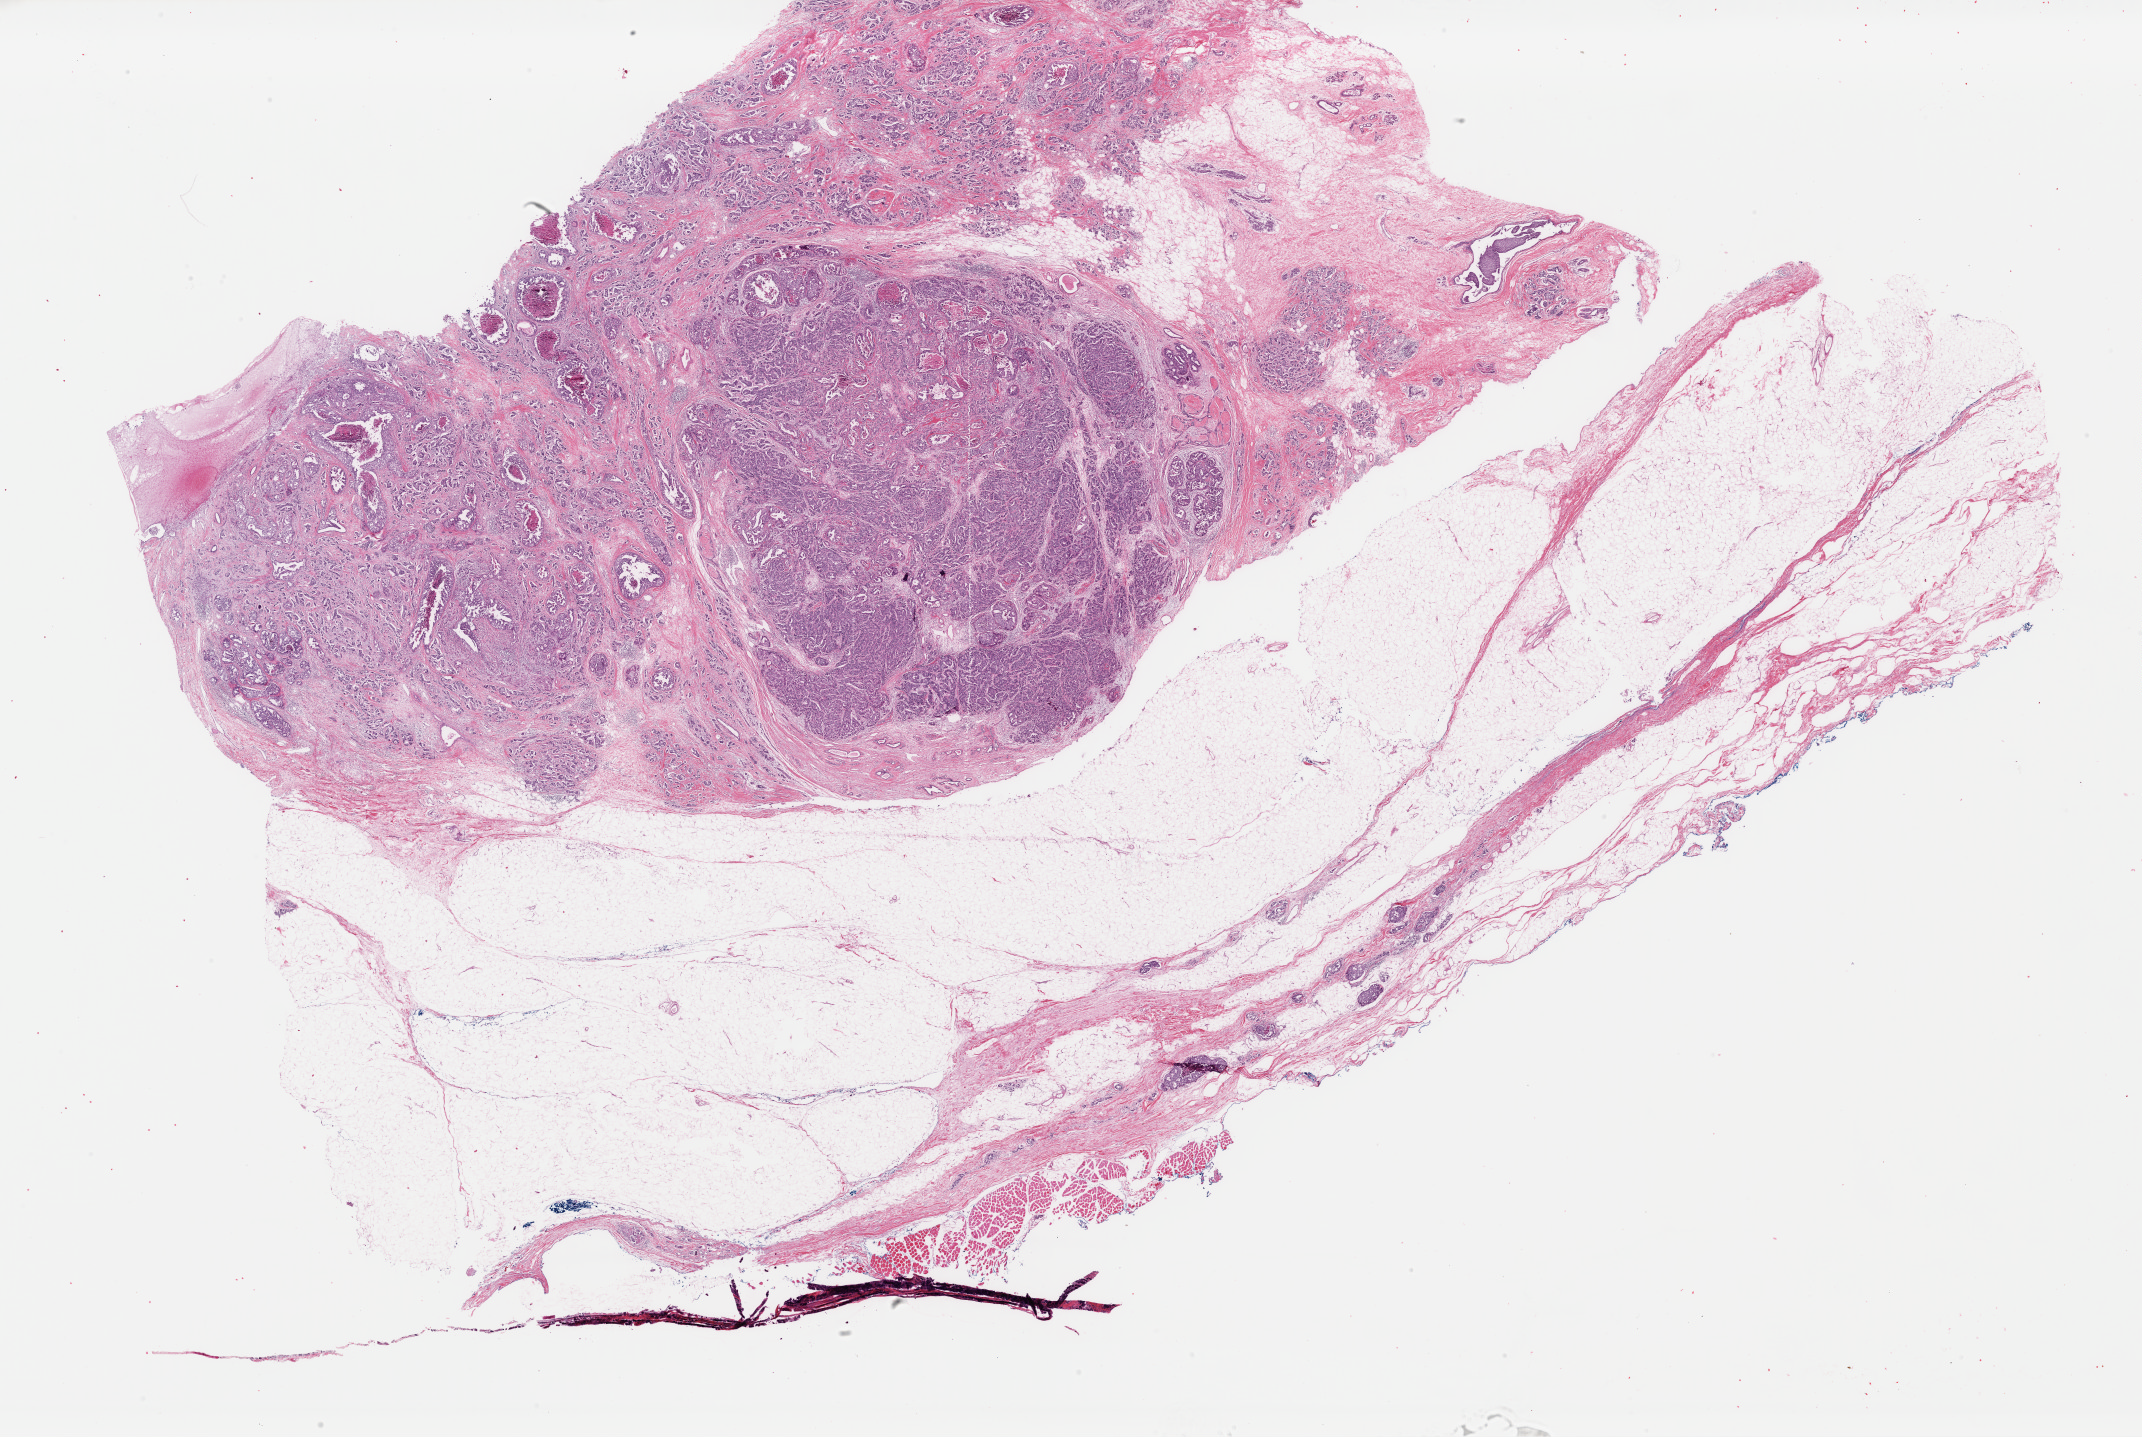
Whole-slide histology image, Hematoxylin and eosin (H&E) stained, shown as a low-resolution overview of the whole scanned area (about 33.8 x 22.7 mm), FFPE section, sample: primary tumour, breast. Female, age 57 years at initial diagnosis.
Lymph nodes positive (case pathology): 24 of 30 examined. Histologic diagnosis: Infiltrating duct carcinoma, NOS. Laterality: right. AJCC pathologic stage: IIIB.